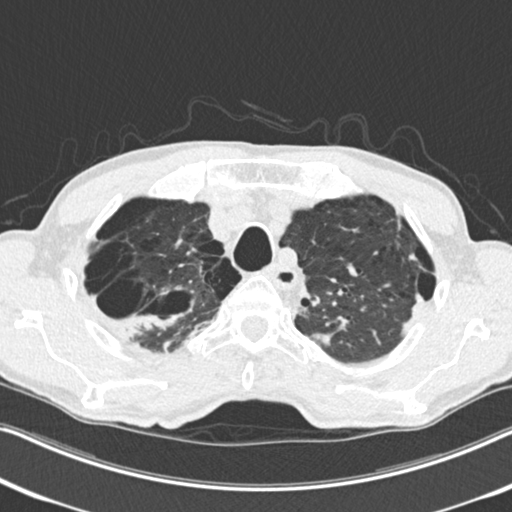
Low-dose screening chest CT, one axial slice. Reconstruction kernel B30f. 120 kVp. Lung window (W 1500 / L -600 HU). 2 mm slice thickness. 512 × 512 image matrix, field of view 334 × 334 mm.
Outlined on this slice (outlined manually by an expert reader):
- lesion 1 (tumor, upper lobe of right lung): bounding box [x1, y1, x2, y2] px = [117, 314, 179, 341]